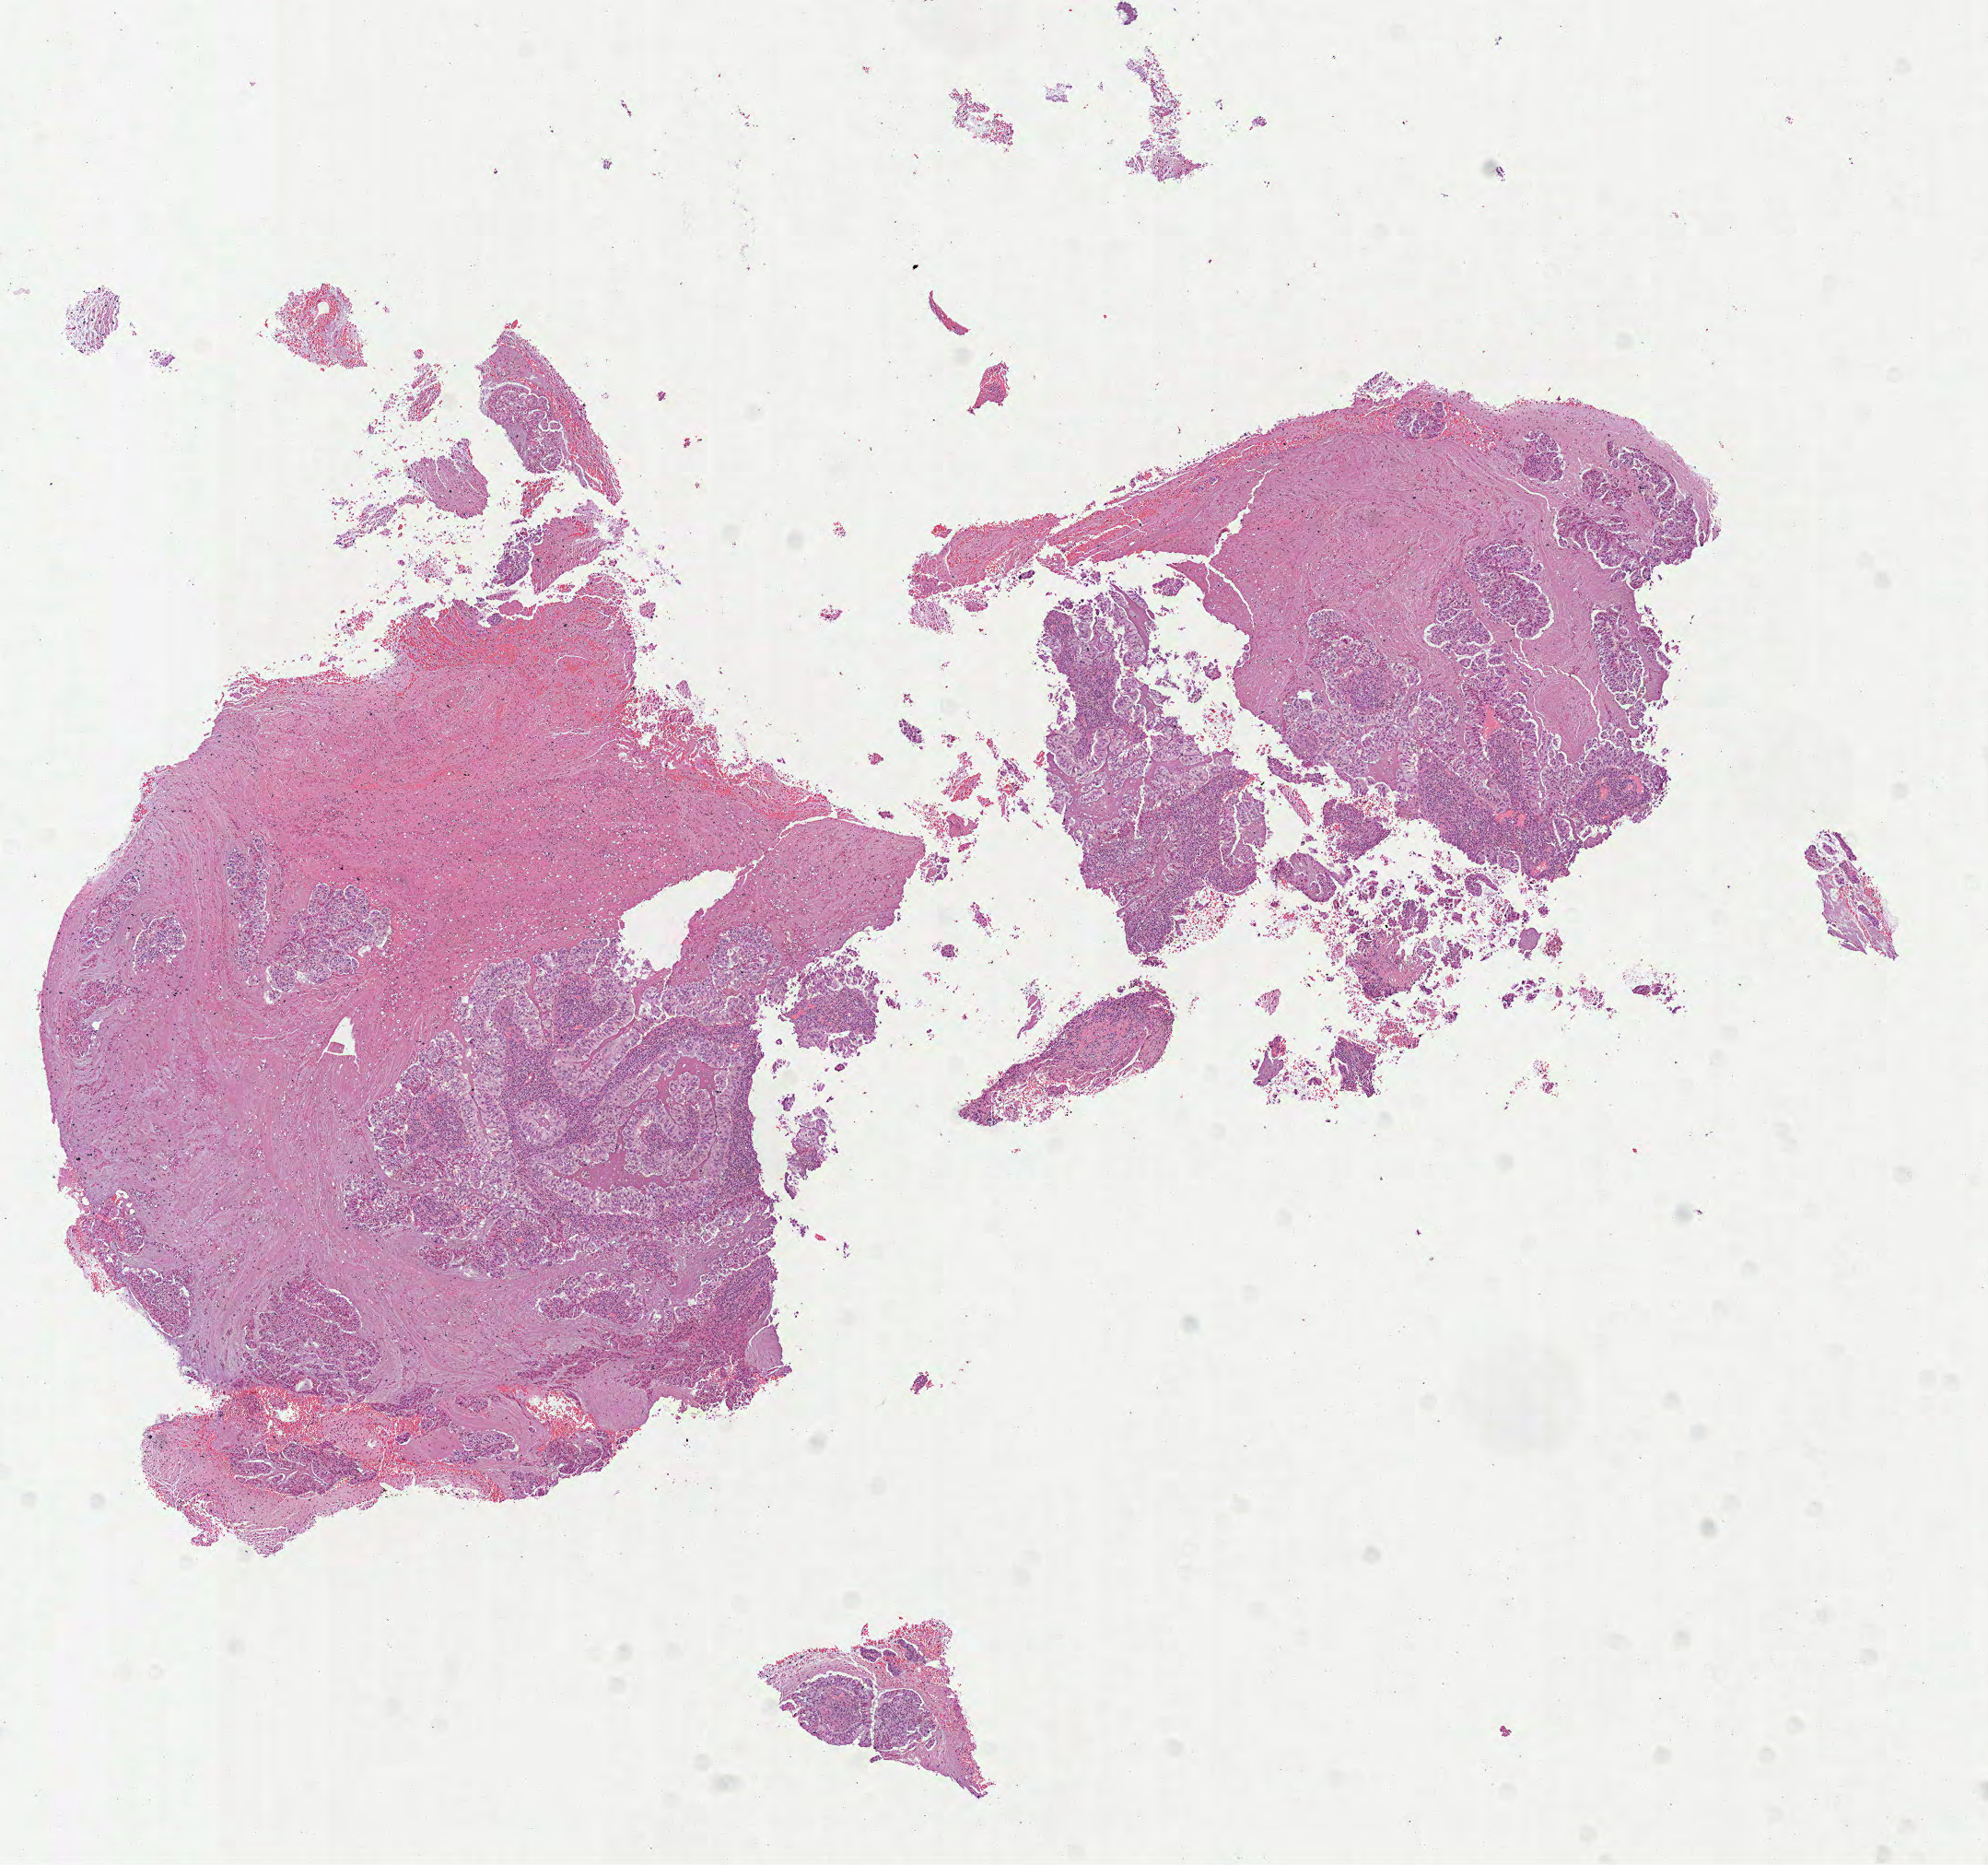
Whole-slide histology image, Hematoxylin and eosin (H&E) stained — shown as a low-resolution overview of the whole scanned area (about 8.7 x 8.2 mm, acquisition: 40x scan). Formalin-fixed paraffin-embedded (FFPE) diagnostic section. Lung, primary tumour sample. Female, age 61 years at initial diagnosis.
• TNM: T1b N0 MX
• diagnosis: Adenocarcinoma, NOS (lower lobe, lung)
• AJCC pathologic stage: IA (7th edition)
• laterality: left